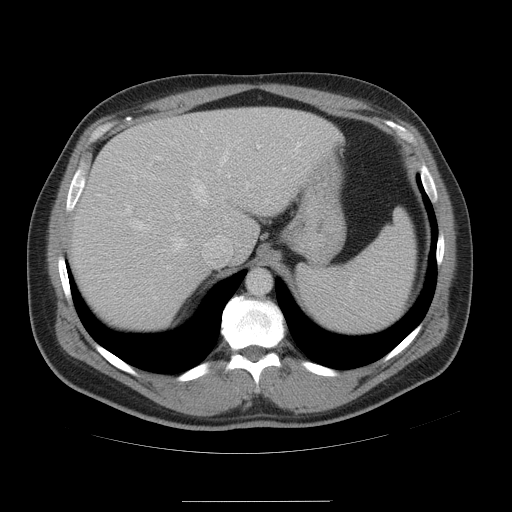
Contrast-enhanced abdominal CT, one axial slice; position 39 of 54 along the scan axis; soft-tissue window (W 400 / L 40 HU); 5 mm slice thickness; 512 × 512 image matrix, field of view 436 × 436 mm. Male patient, age 40 years. Case-level facts recorded for this patient, not image findings: diagnosis: colorectal cancer liver metastases, imaged before liver resection; multiple liver metastases: no; largest metastasis: 15 cm.
Outlined on this slice (expert manual segmentation):
- hepatic veins: box from (x=119, y=152) to (x=230, y=268) px
- liver: (x=71, y=108)–(x=343, y=331)
- planned liver remnant (the part of the liver to remain after resection): (x=176, y=107)–(x=343, y=274)
- portal vein (with intrahepatic branches): (x=148, y=135)–(x=243, y=166)